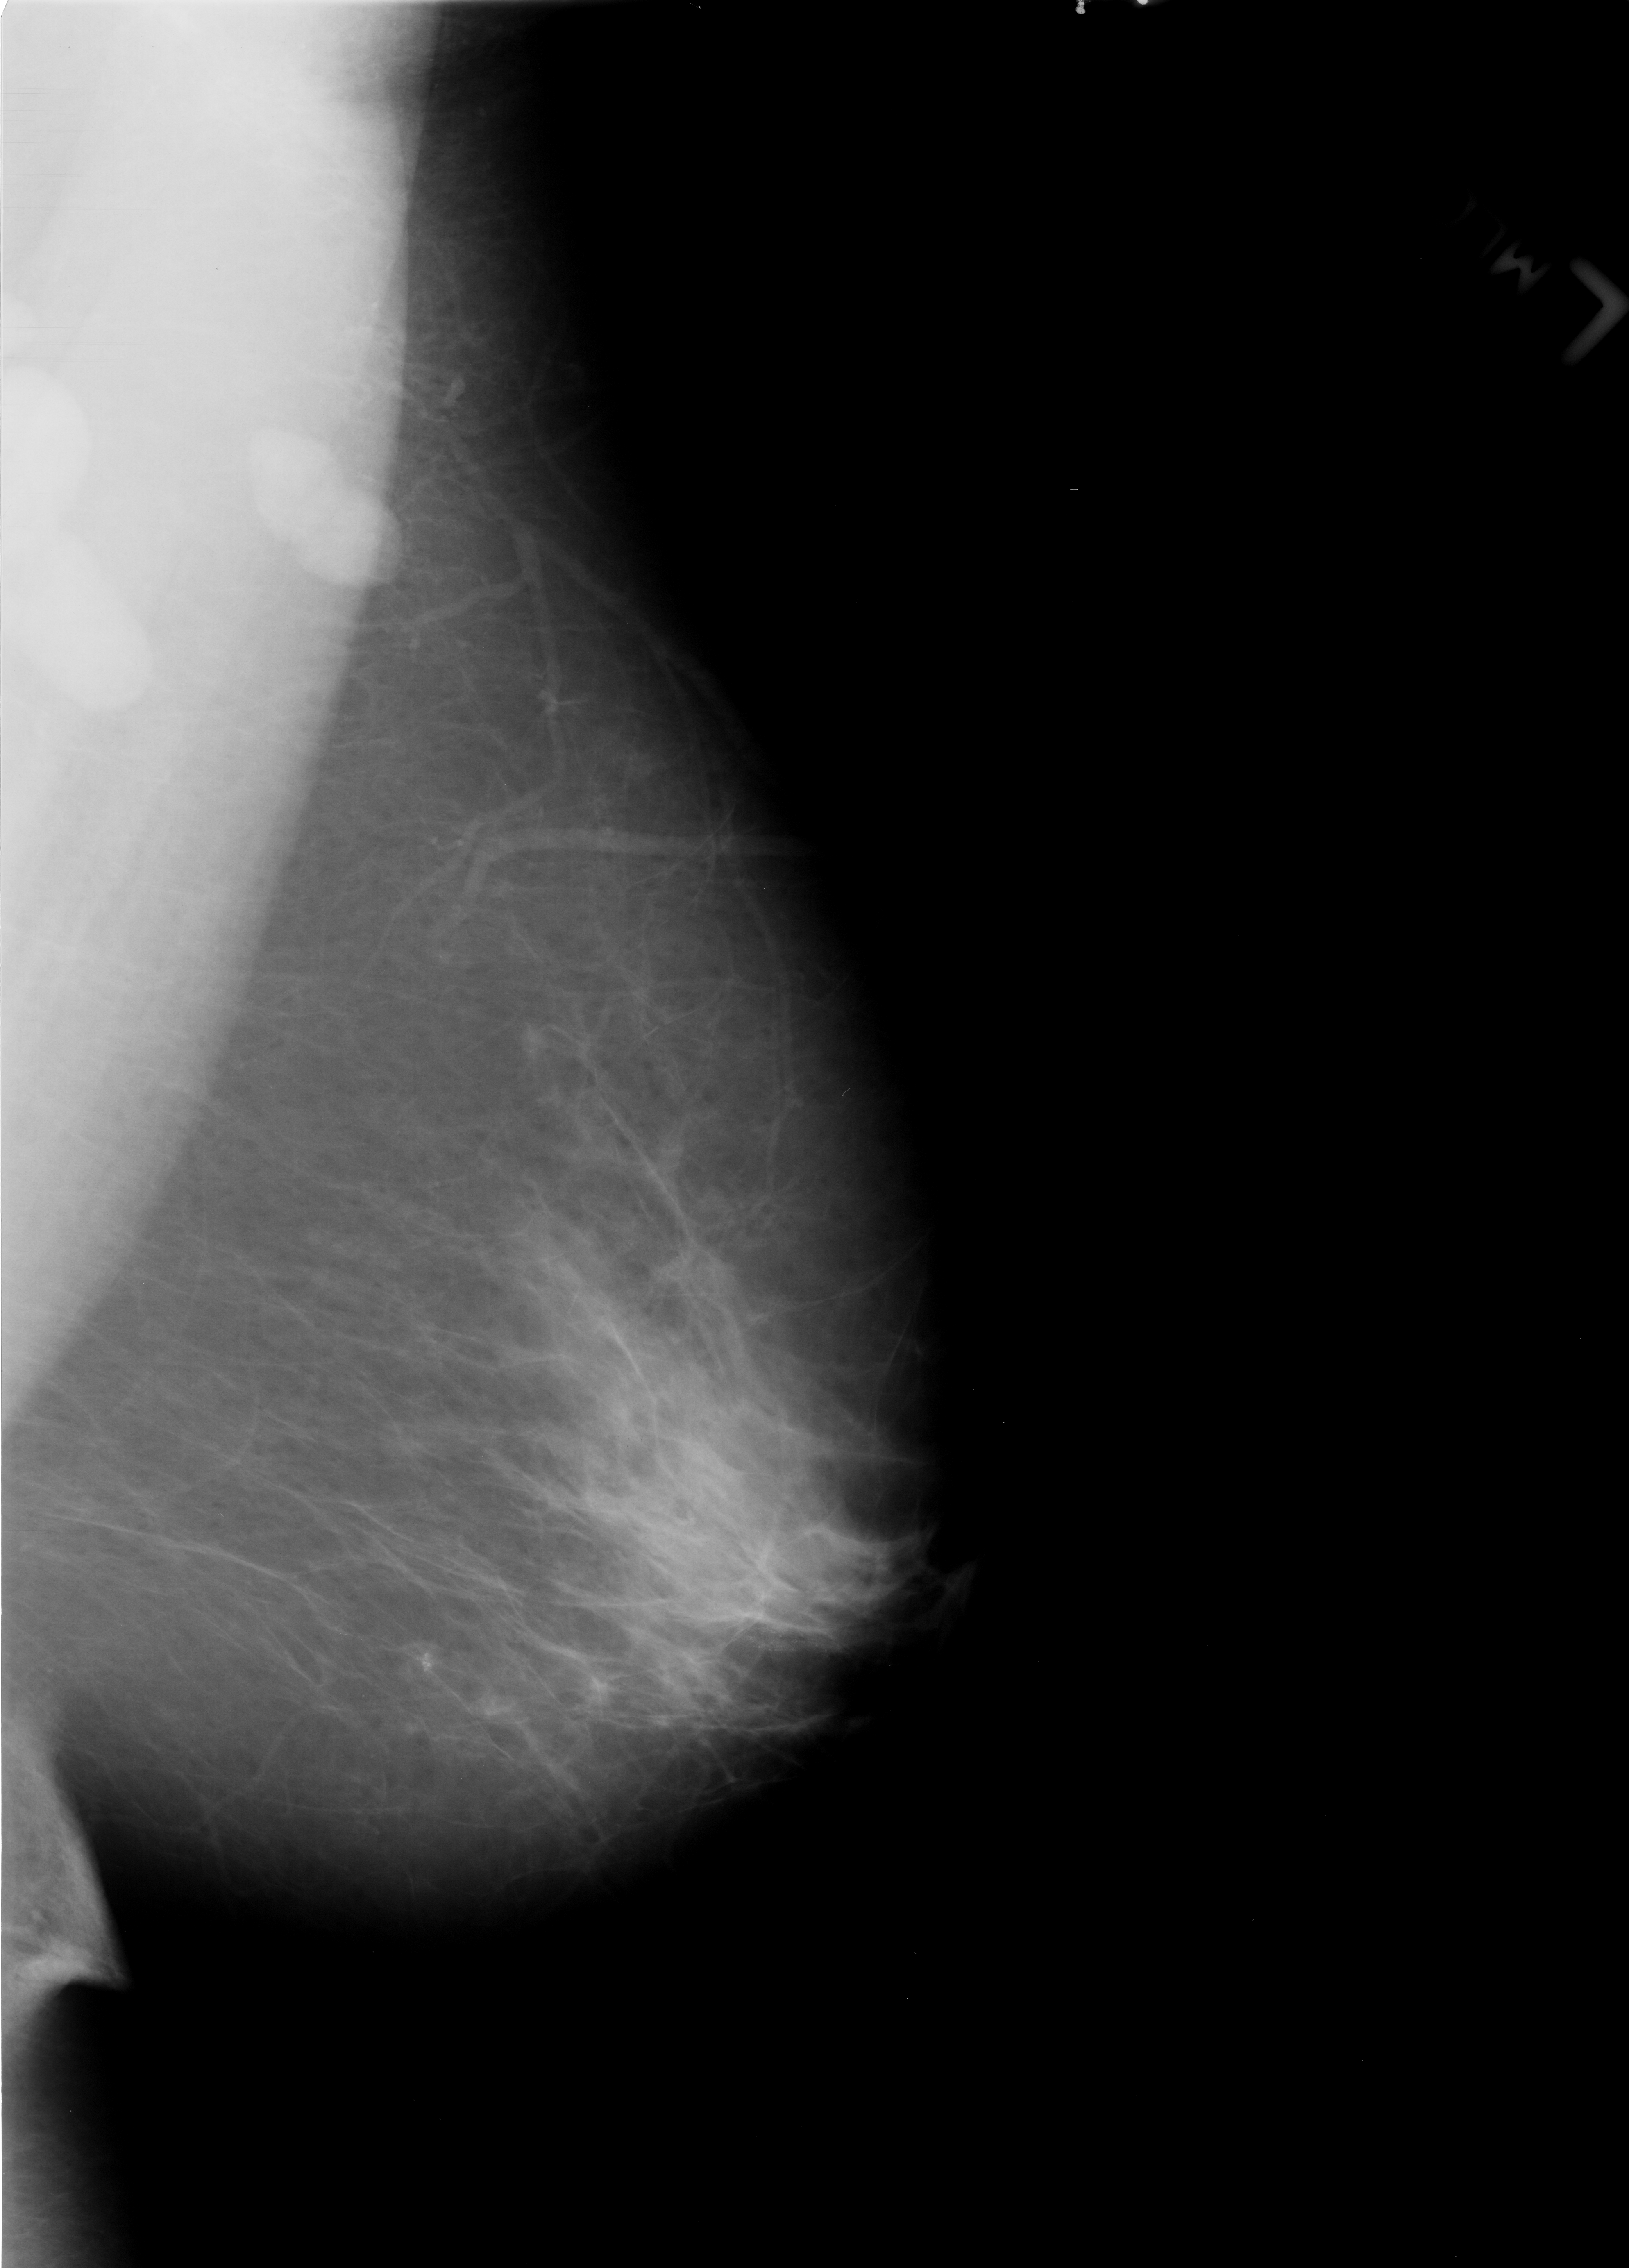
Digitized screen-film mammogram, left breast, MLO view, breast composition: scattered fibroglandular densities (BI-RADS density category 2 of 4).
Marked findings (only marked abnormalities are described; nothing is implied about the rest of the image): Finding 1 of 2: calcifications, morphology fine linear branching, distribution clustered / linear; BI-RADS assessment category 4; subtlety rating 2 on a 1 (subtle) to 5 (obvious) scale; pathology (as recorded): benign. Finding 2 of 2: calcifications, morphology pleomorphic, distribution clustered; BI-RADS assessment category 4; pathology result (as recorded, not read from the image): benign.